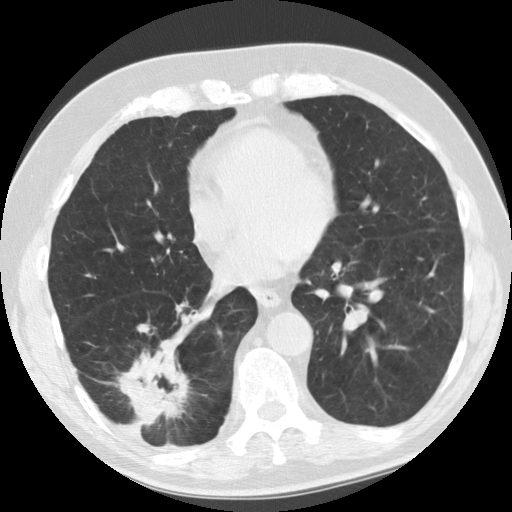
Chest CT (low-dose screening protocol), one axial image; baseline annual screen; lung window (W 1500 / L -600 HU); slice 87 of 135 in the series; 512 × 512 image matrix. Male participant, aged 69 years at enrolment.
Lesion marked by an expert reader, bounding box [x1, y1, x2, y2] px = [109, 332, 195, 441]. The screening reader recorded 2 non-calcified nodules or masses ≥4 mm on this exam (right lower lobe, right lower lobe); which of them this box marks is not recorded. Later outcome: lung cancer diagnosed 40 days after this screen — adenocarcinoma, NOS, right lower lobe, stage IIB (AJCC 6th edition), 45 mm at pathology.